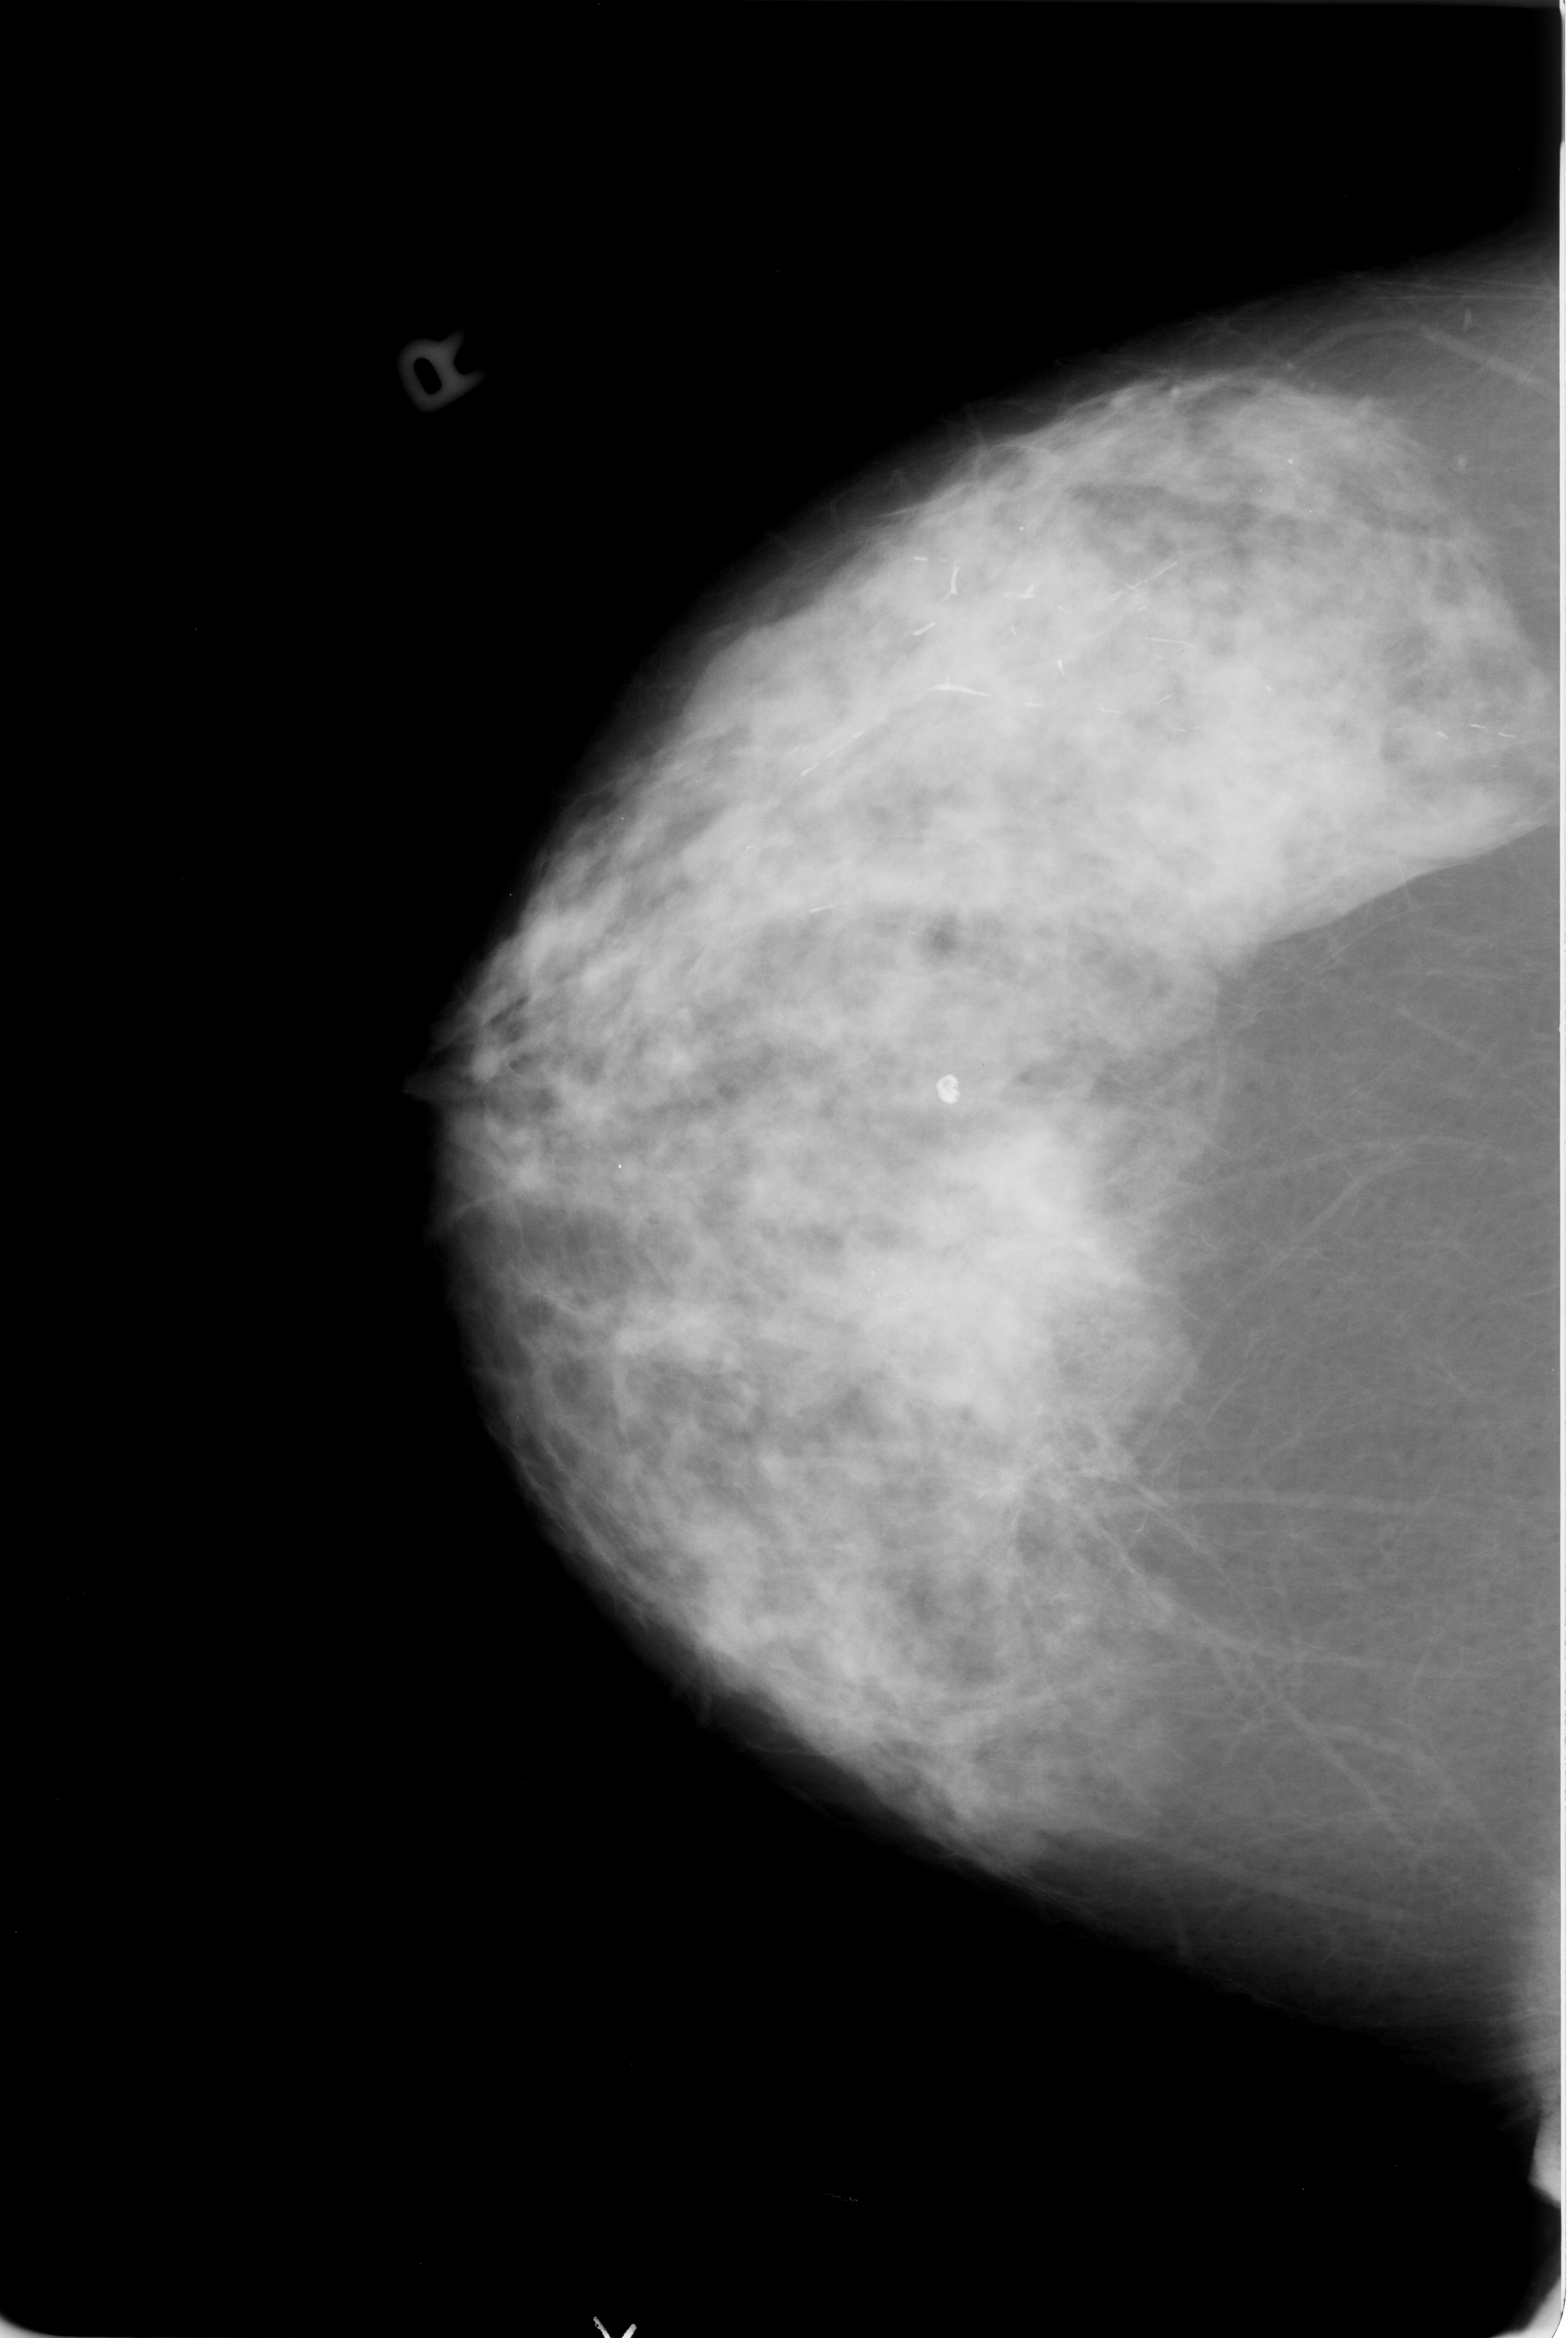
Digitized screen-film mammogram, right breast, CC view, breast composition: heterogeneously dense (BI-RADS density category 3 of 4).
Marked findings (only marked abnormalities are described; nothing is implied about the rest of the image): mass, shape architectural distortion, margins ill defined; BI-RADS assessment category 4; pathology (as recorded): malignant.